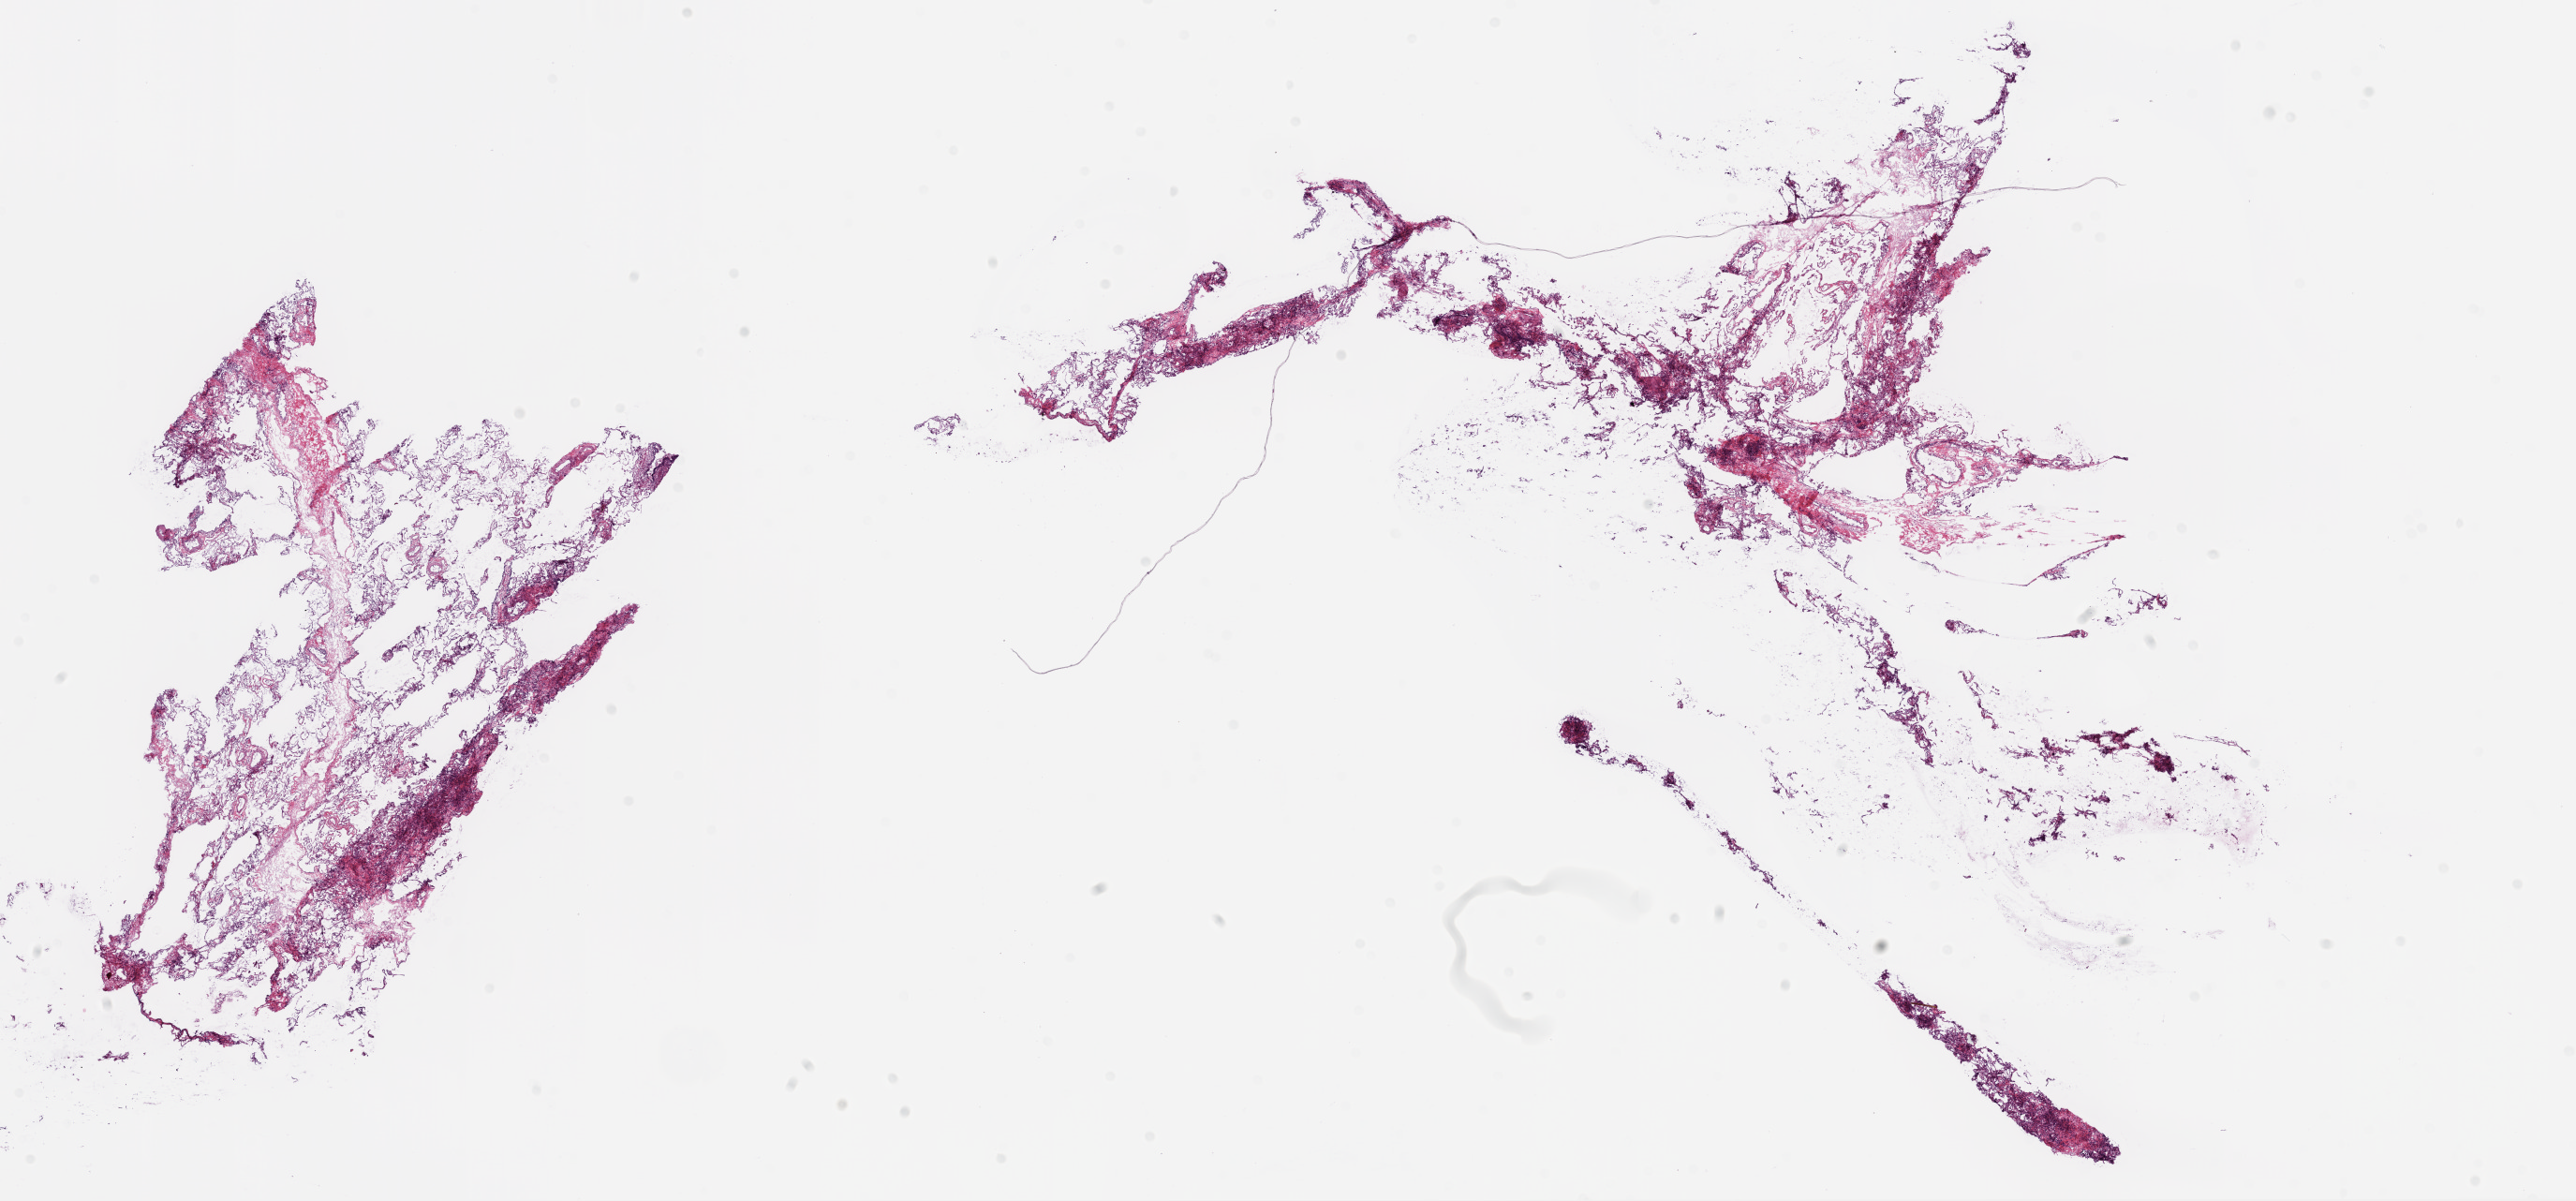
Hematoxylin and eosin (H&E) stained whole-slide image — shown as a low-resolution overview of the whole scanned area (about 22.1 x 10.3 mm), frozen section from the bottom of the tissue portion, lung, solid tissue normal (non-tumour tissue) sample. Female patient; age at initial diagnosis 74 years.
This section: solid tissue normal sample (biorepository sample class). Patient diagnosis: Squamous cell carcinoma, NOS.